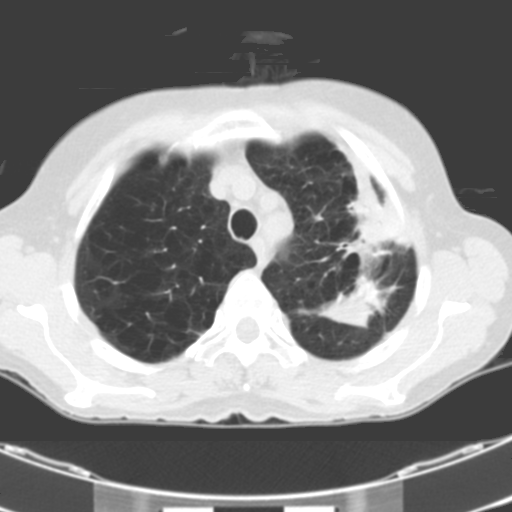
Low-dose screening chest CT, one axial slice; one of 2 acquisitions stored at this slice position; lung window (W 1500 / L -600 HU); 512 × 512 image matrix, field of view 299 × 299 mm.
Outlined on this slice (outlined manually by an expert reader):
- lesion 1 (tumor): bounding box [x1, y1, x2, y2] px = [320, 297, 371, 327]